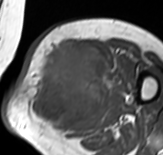
MRI of an extremity soft-tissue mass, one axial slice. Position 40 of 65 along the scan axis. MR volume resampled by the dataset authors to the PET/CT grid (not the native acquisition matrix). 3.27 mm slice thickness. 163 × 155 image matrix, field of view 159 × 151 mm. Female patient. Case-level facts recorded for this patient, not image findings: histological type: pleomorphic leiomyosarcoma; grade: high; site of the primary tumour: left thigh.
Structures marked on this image (expert contour drawn on MRI and transferred to this co-registered scan by the dataset authors):
- gross tumour volume including surrounding oedema: bounding box [x1, y1, x2, y2] px = [30, 40, 106, 134]
- gross tumour volume (mass): [37, 40, 106, 123]